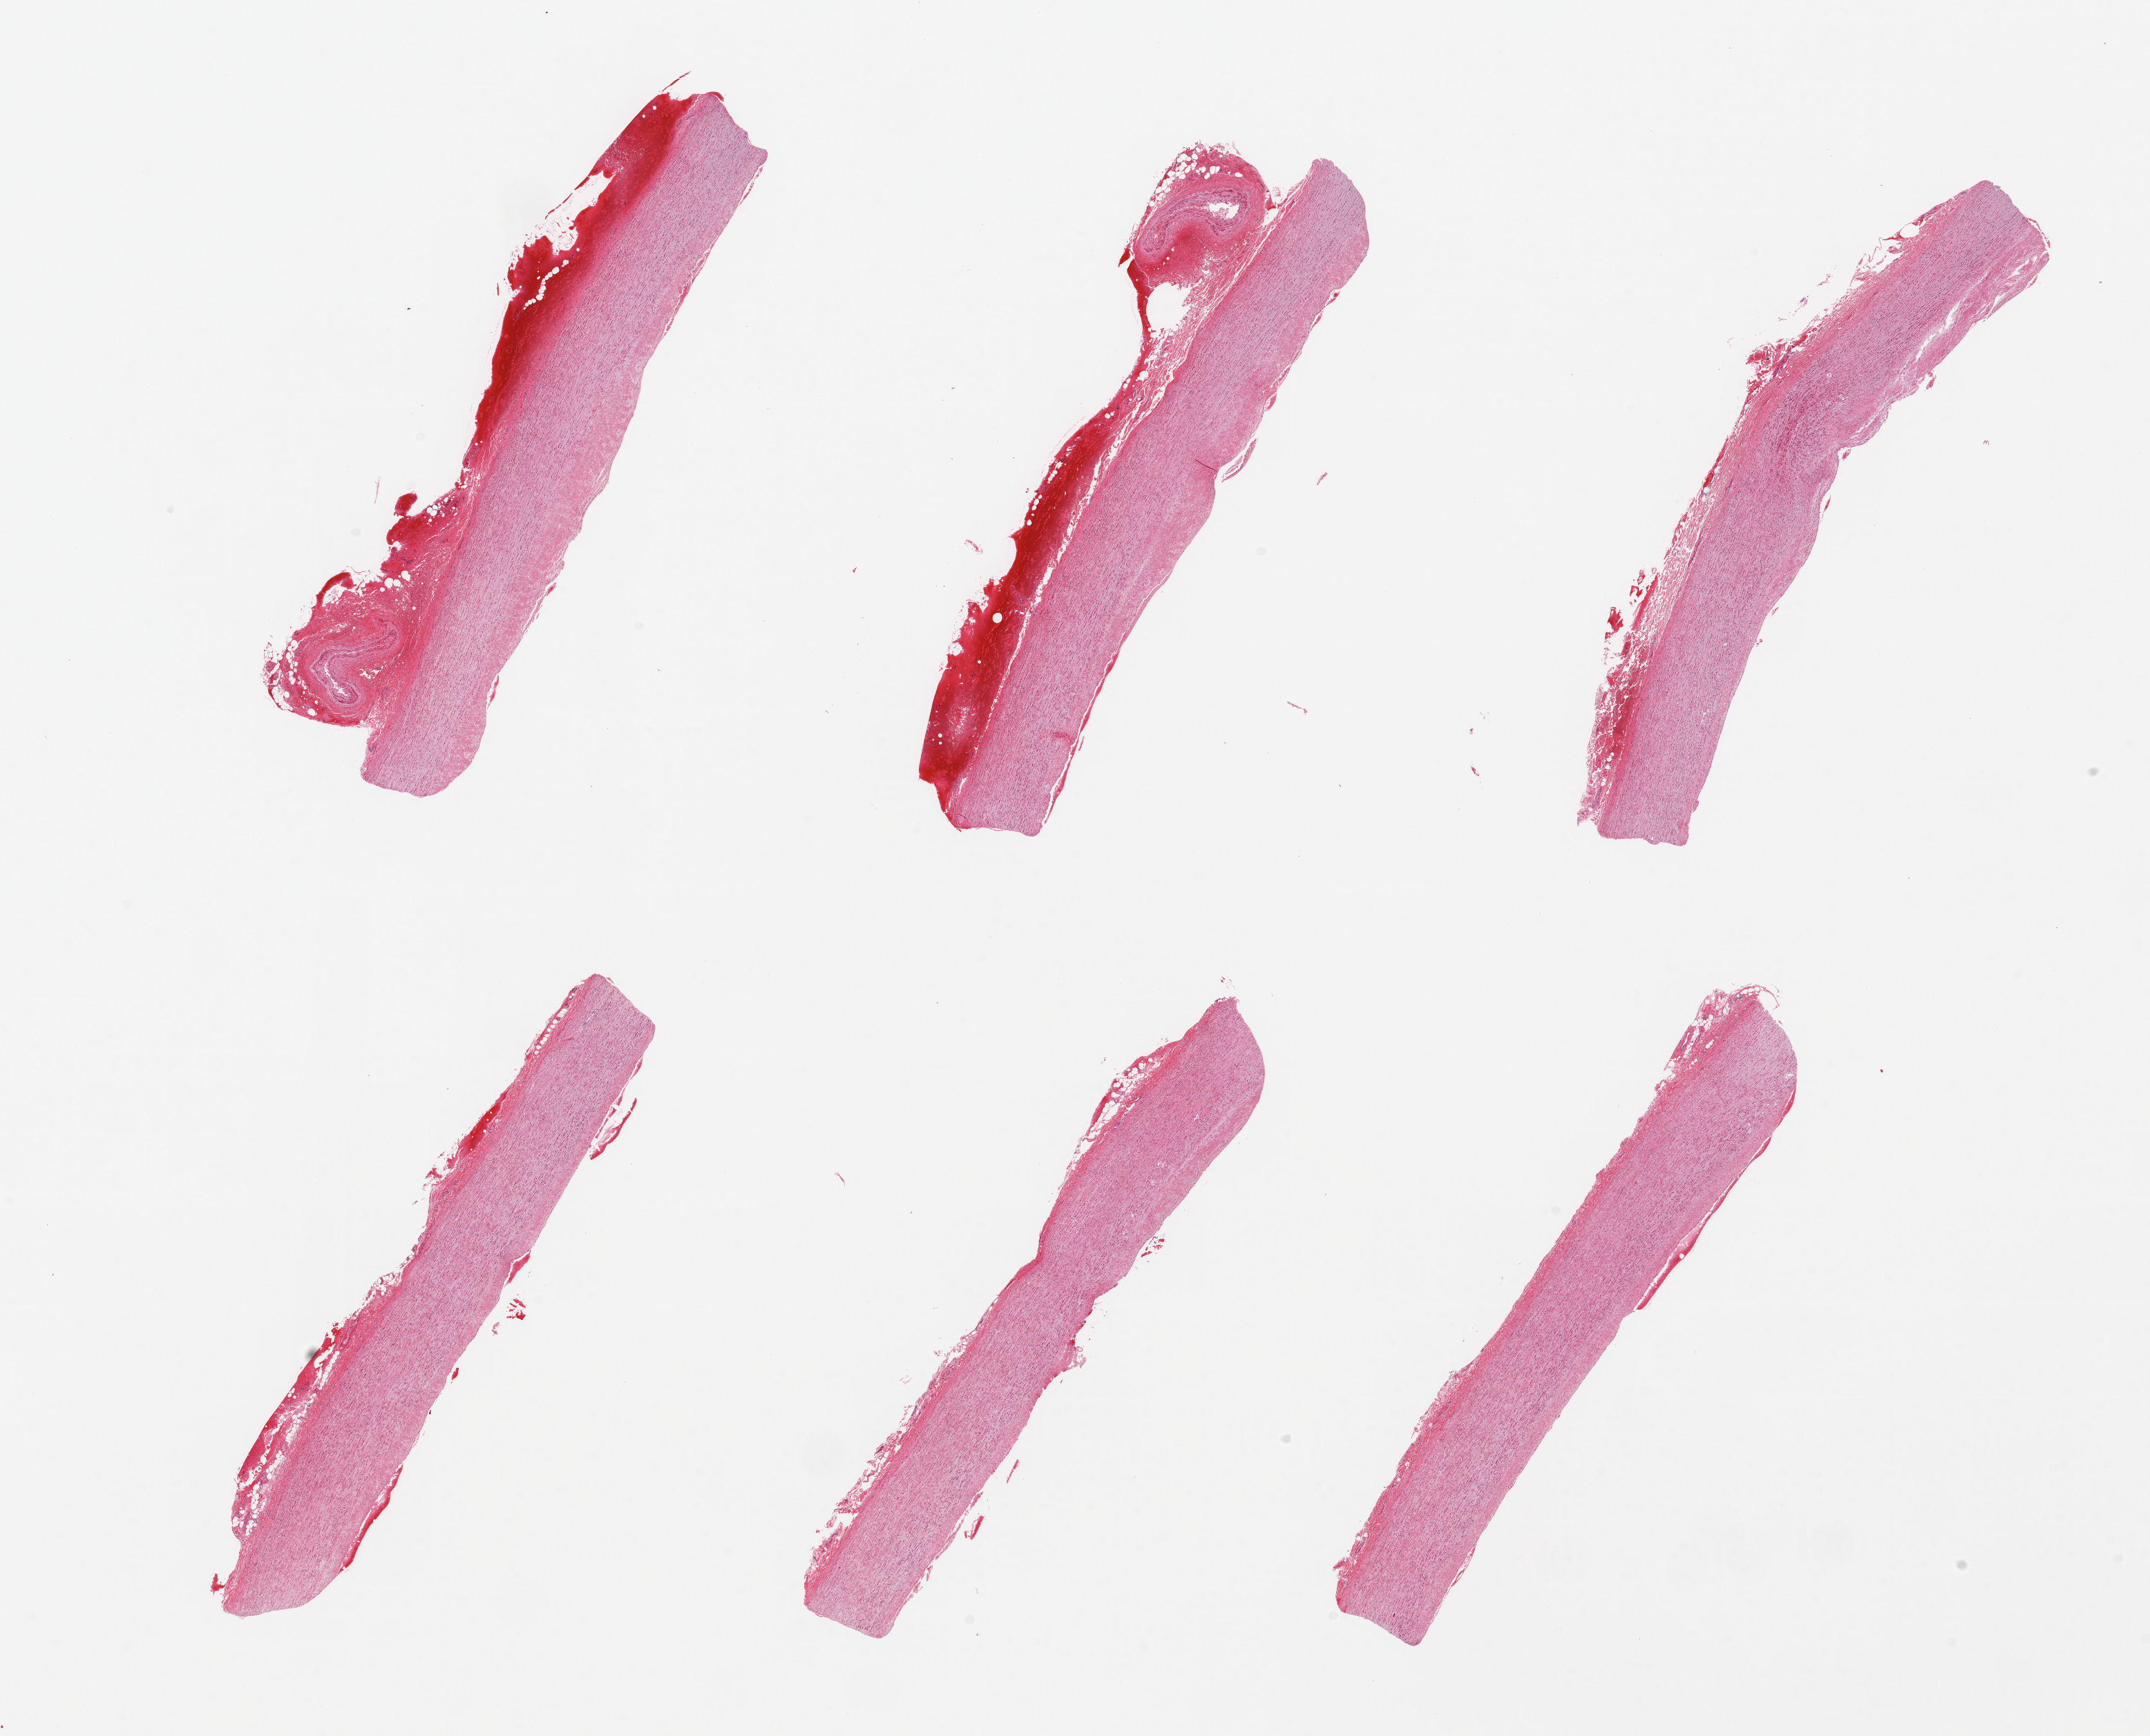
Digitized H&E-stained section, whole scanned area (about 24.6 x 19.9 mm, from a 20x scan) shown as a low-resolution overview; PAXgene-fixed, paraffin-embedded tissue; sampled site (target tissue): aorta; donor tissue sample.
* review note (as recorded): 6 pieces, atherosis up to ~0.3mm